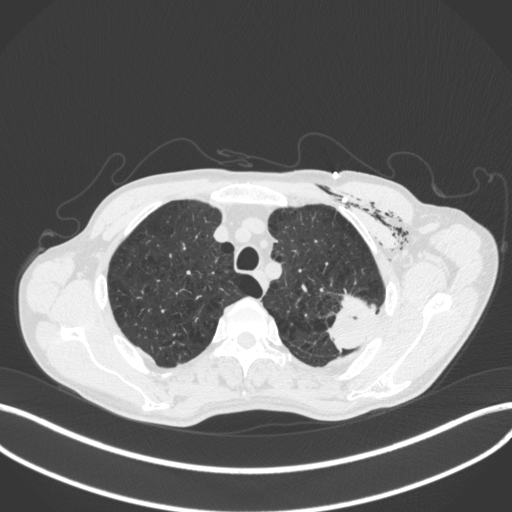
Chest CT, one axial slice; reconstruction kernel B31f; 120 kVp; lung window (W 1500 / L -600 HU); 1 mm slice thickness; 512 × 512 image matrix, field of view 400 × 400 mm. Patient: male, 58 years. From the clinical record (not read from this slice): clinical TNM (as recorded): T3 N0 M0.
Annotated regions visible in this slice (rectangle marked by the reading radiologist):
- lung tumour (recorded histology: adenocarcinoma): bounding box <317,288,385,353> (left, top, right, bottom; pixels)